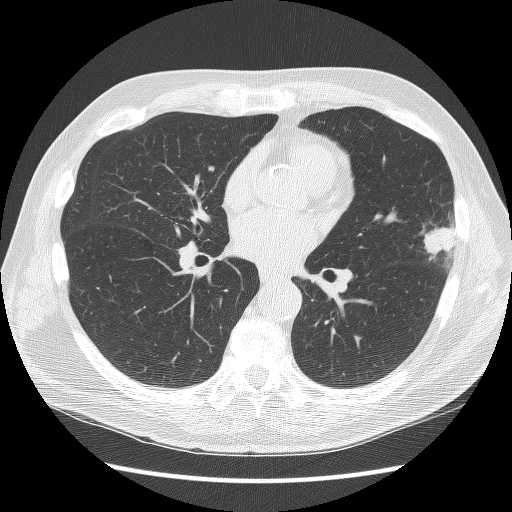
Axial slice from a low-dose chest CT screening exam. Third screening round (two years after baseline). Lung window (W 1500 / L -600 HU). 2.5 mm slice thickness. Lung (sharp) reconstruction kernel (BONE). Male, age 67 years at enrolment. Former smoker at enrolment.
• Expert reader's lesion annotation, box from (x=408, y=205) to (x=474, y=277) px.
• The exam's reader record, not a measurement of the box and not confirmed to be the same lesion: non-calcified nodule or mass ≥4 mm, left upper lobe, 22 × 17 mm, poorly defined margins, soft tissue attenuation, pre-existing on the prior screen: yes; interval growth: yes.
• Later outcome: lung cancer diagnosed 72 days after this screen — squamous cell carcinoma, NOS, left upper lobe, moderately differentiated (G2), stage IB (AJCC 6th edition), 25 mm at pathology.